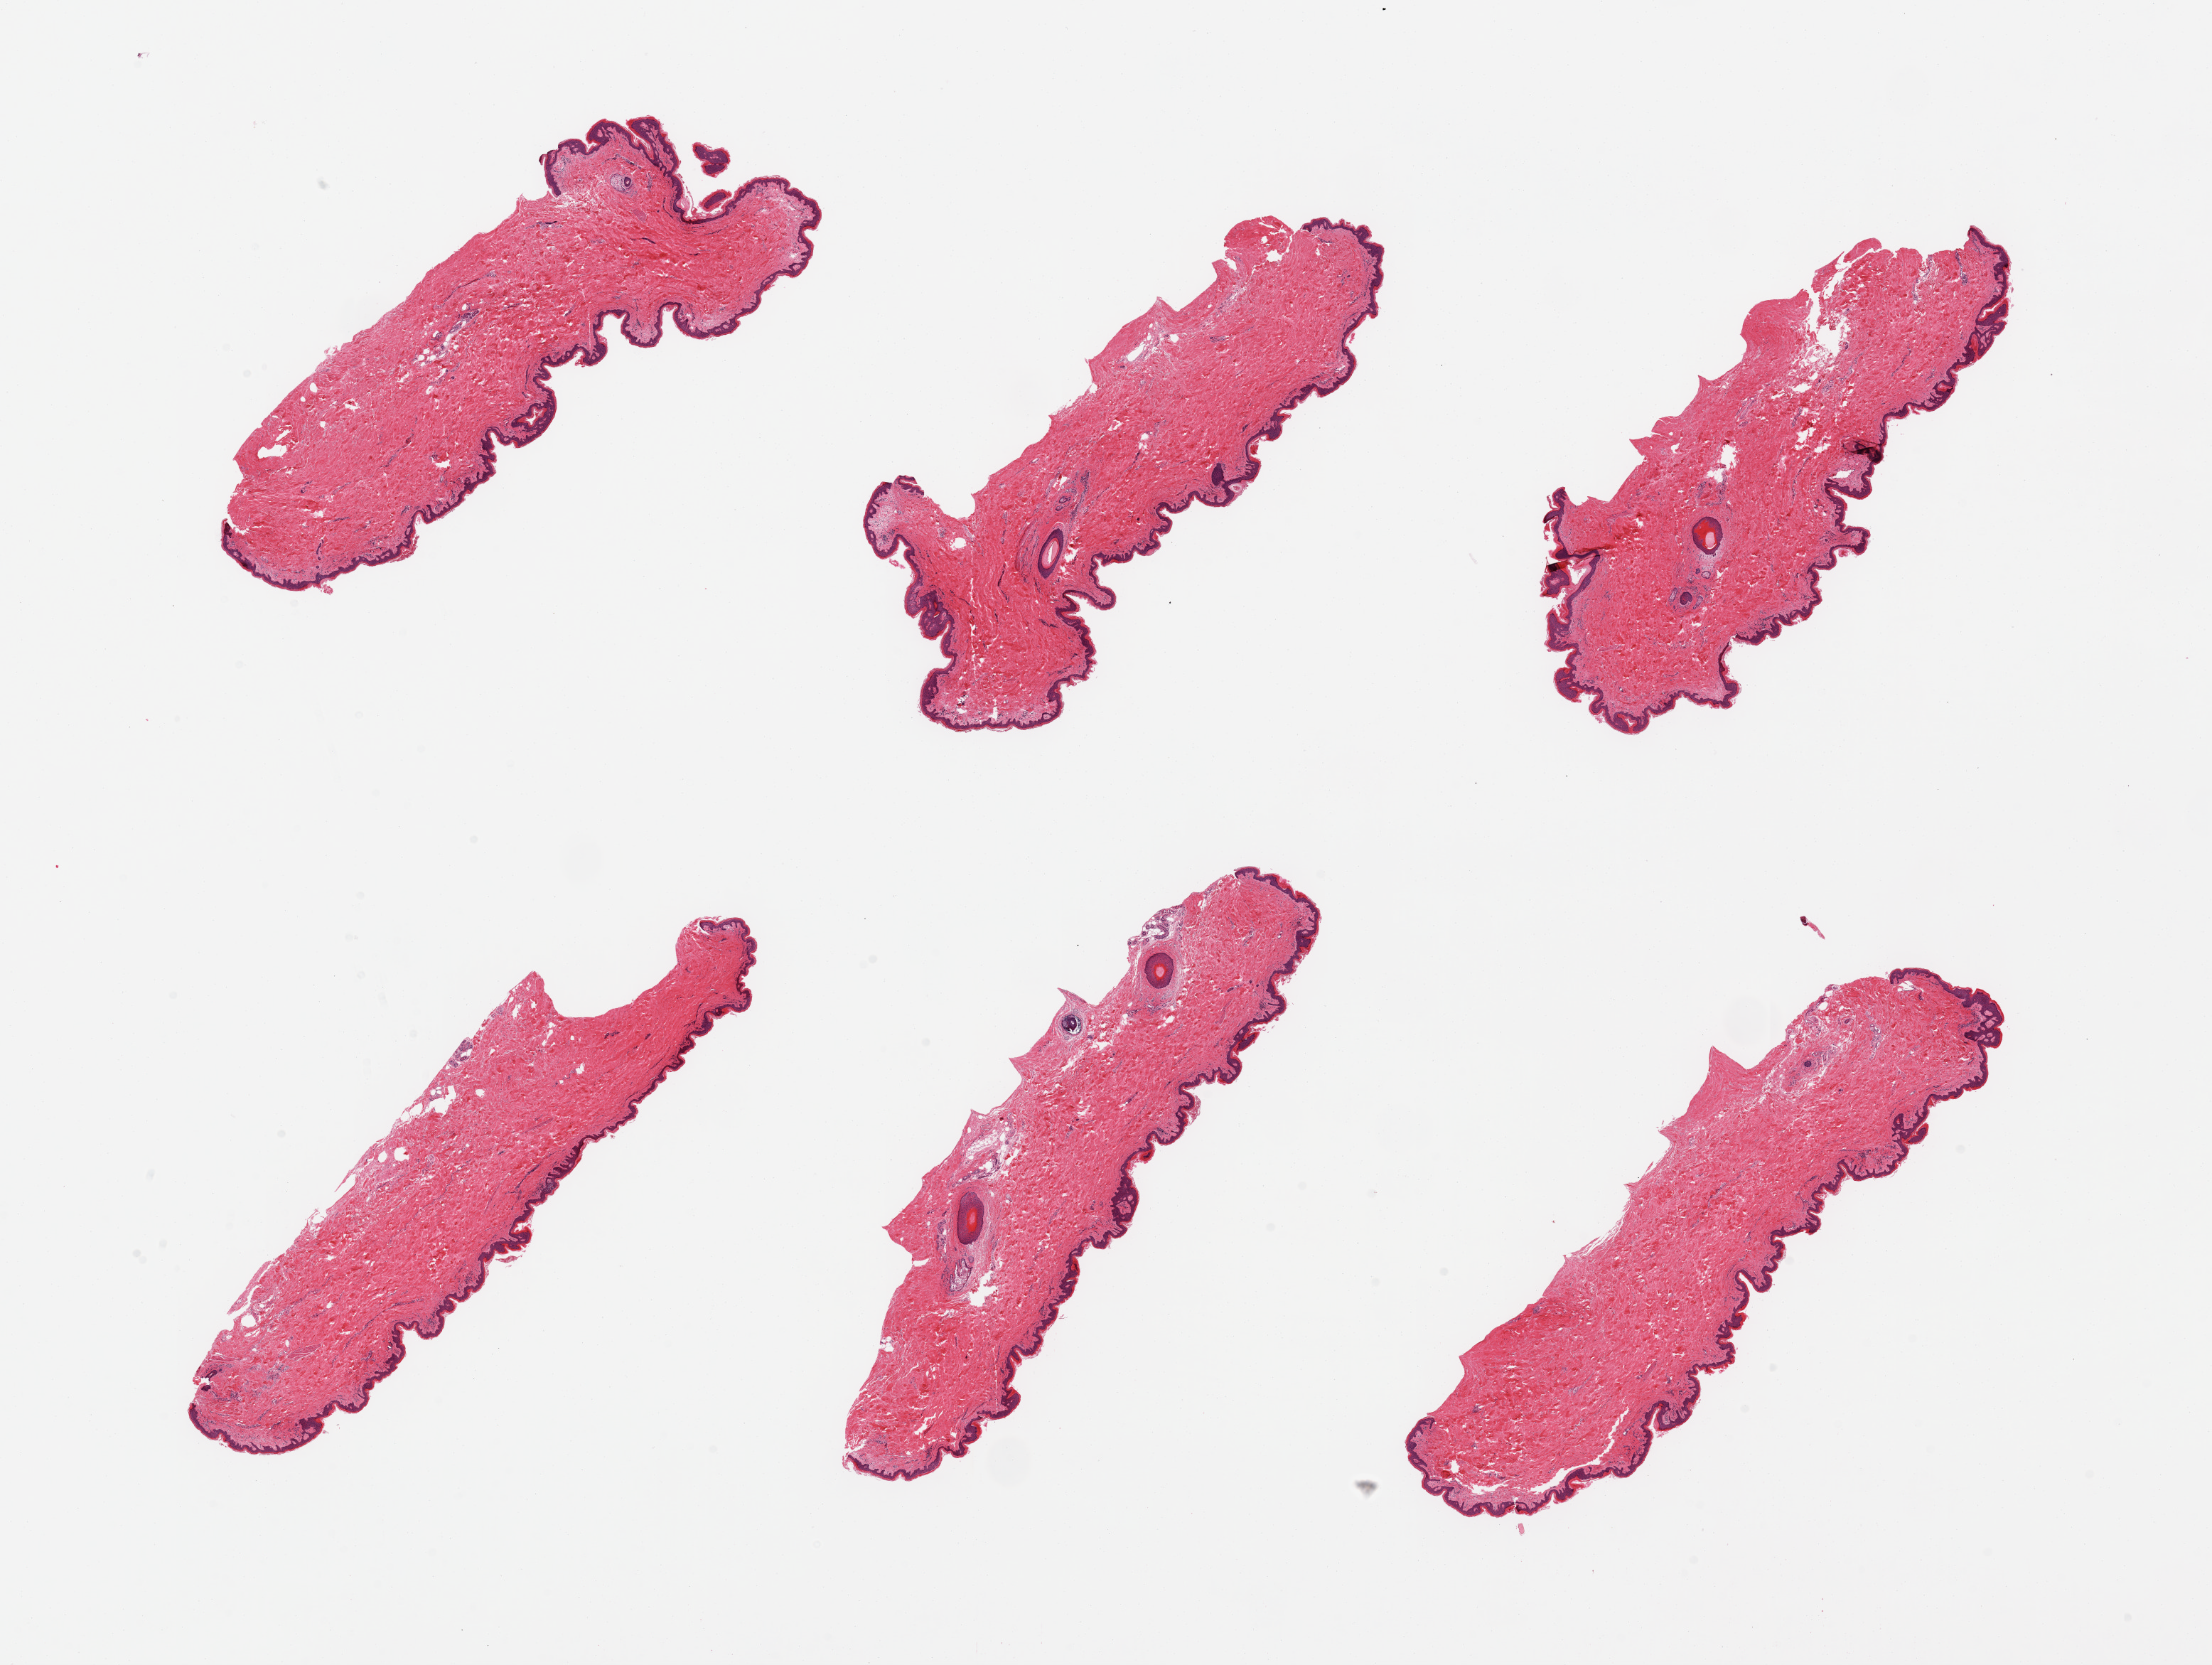
Haematoxylin and eosin whole-slide image, whole scanned area (about 24.6 x 18.5 mm, slide scanned at 20x) shown as a low-resolution overview, PAXgene-fixed paraffin-embedded (PFPE) section, sampled site (target tissue): skin of suprapubic region, donor tissue sample.
Review note (as recorded): 6 pieces; well trimmed.